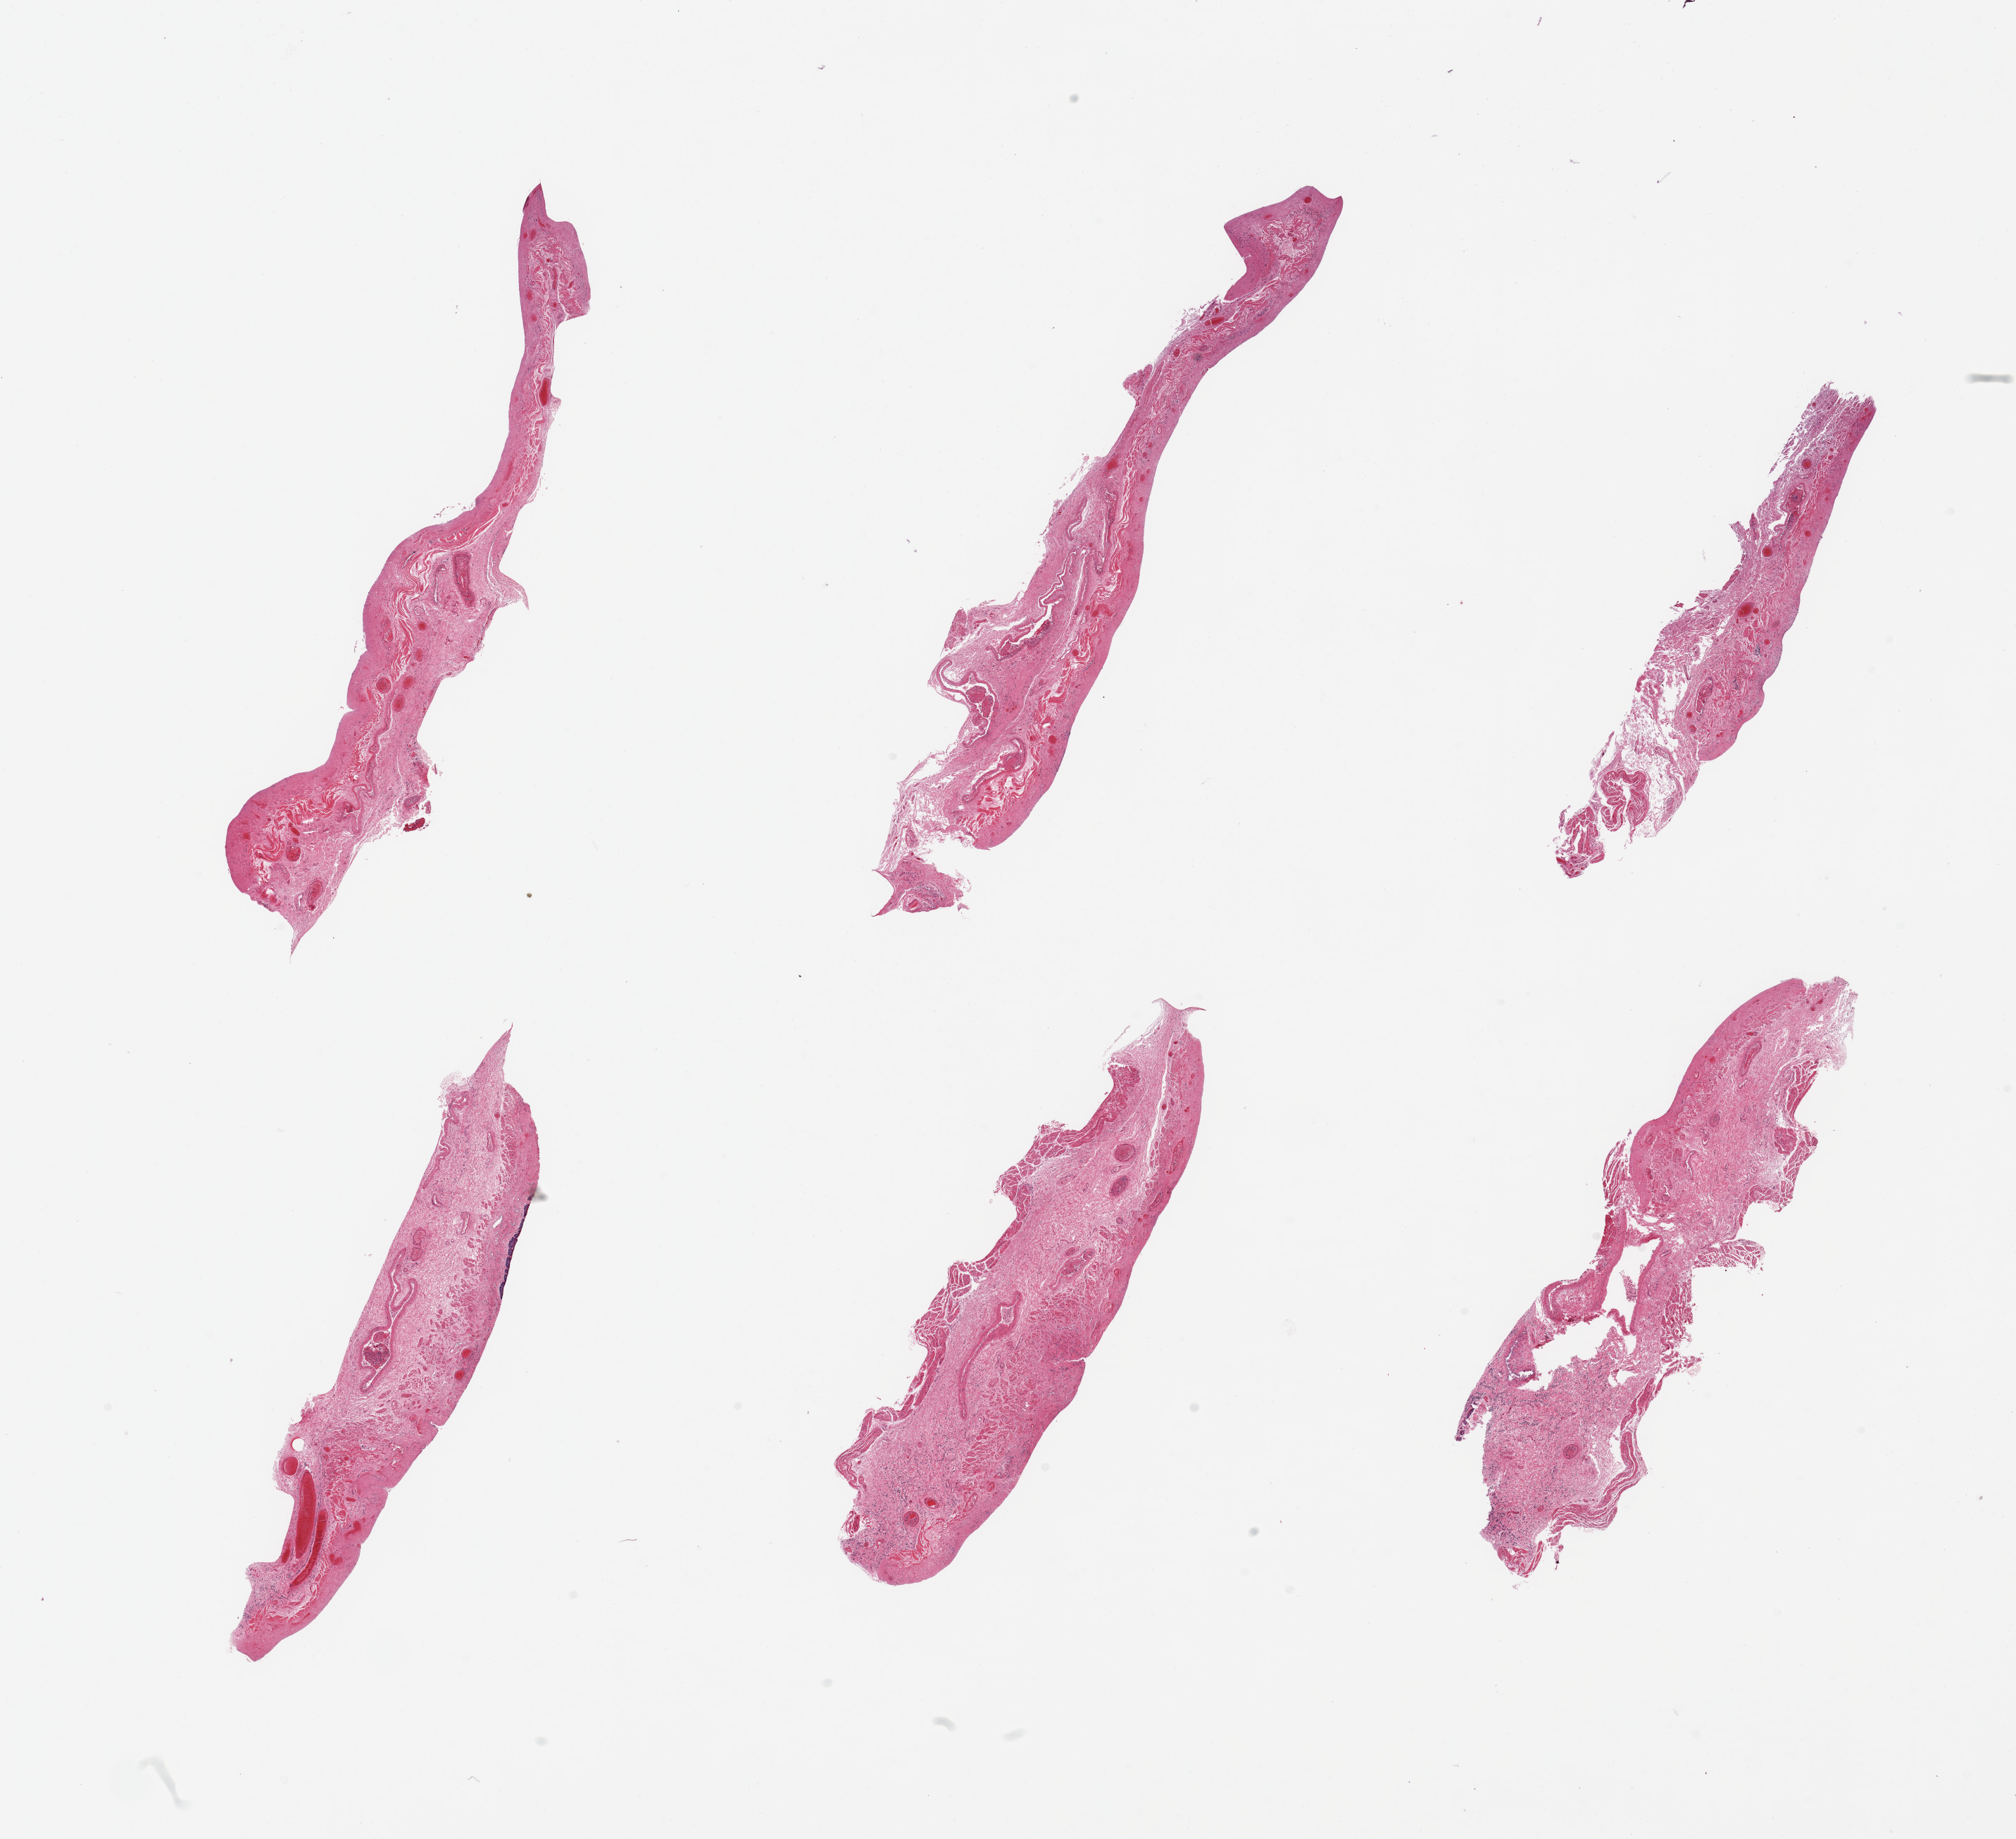
Digitized H&E-stained section, brightfield — low-resolution overview of the scanned area, about 22.6 x 20.7 mm, PAXgene-fixed paraffin-embedded (PFPE) section, target tissue: esophageal mucous membrane, donor tissue sample. Donor sex: female.
Review note (as recorded): 6 pieces, target squamous mucosa largely sloughed, residual islands up <0.1mm.